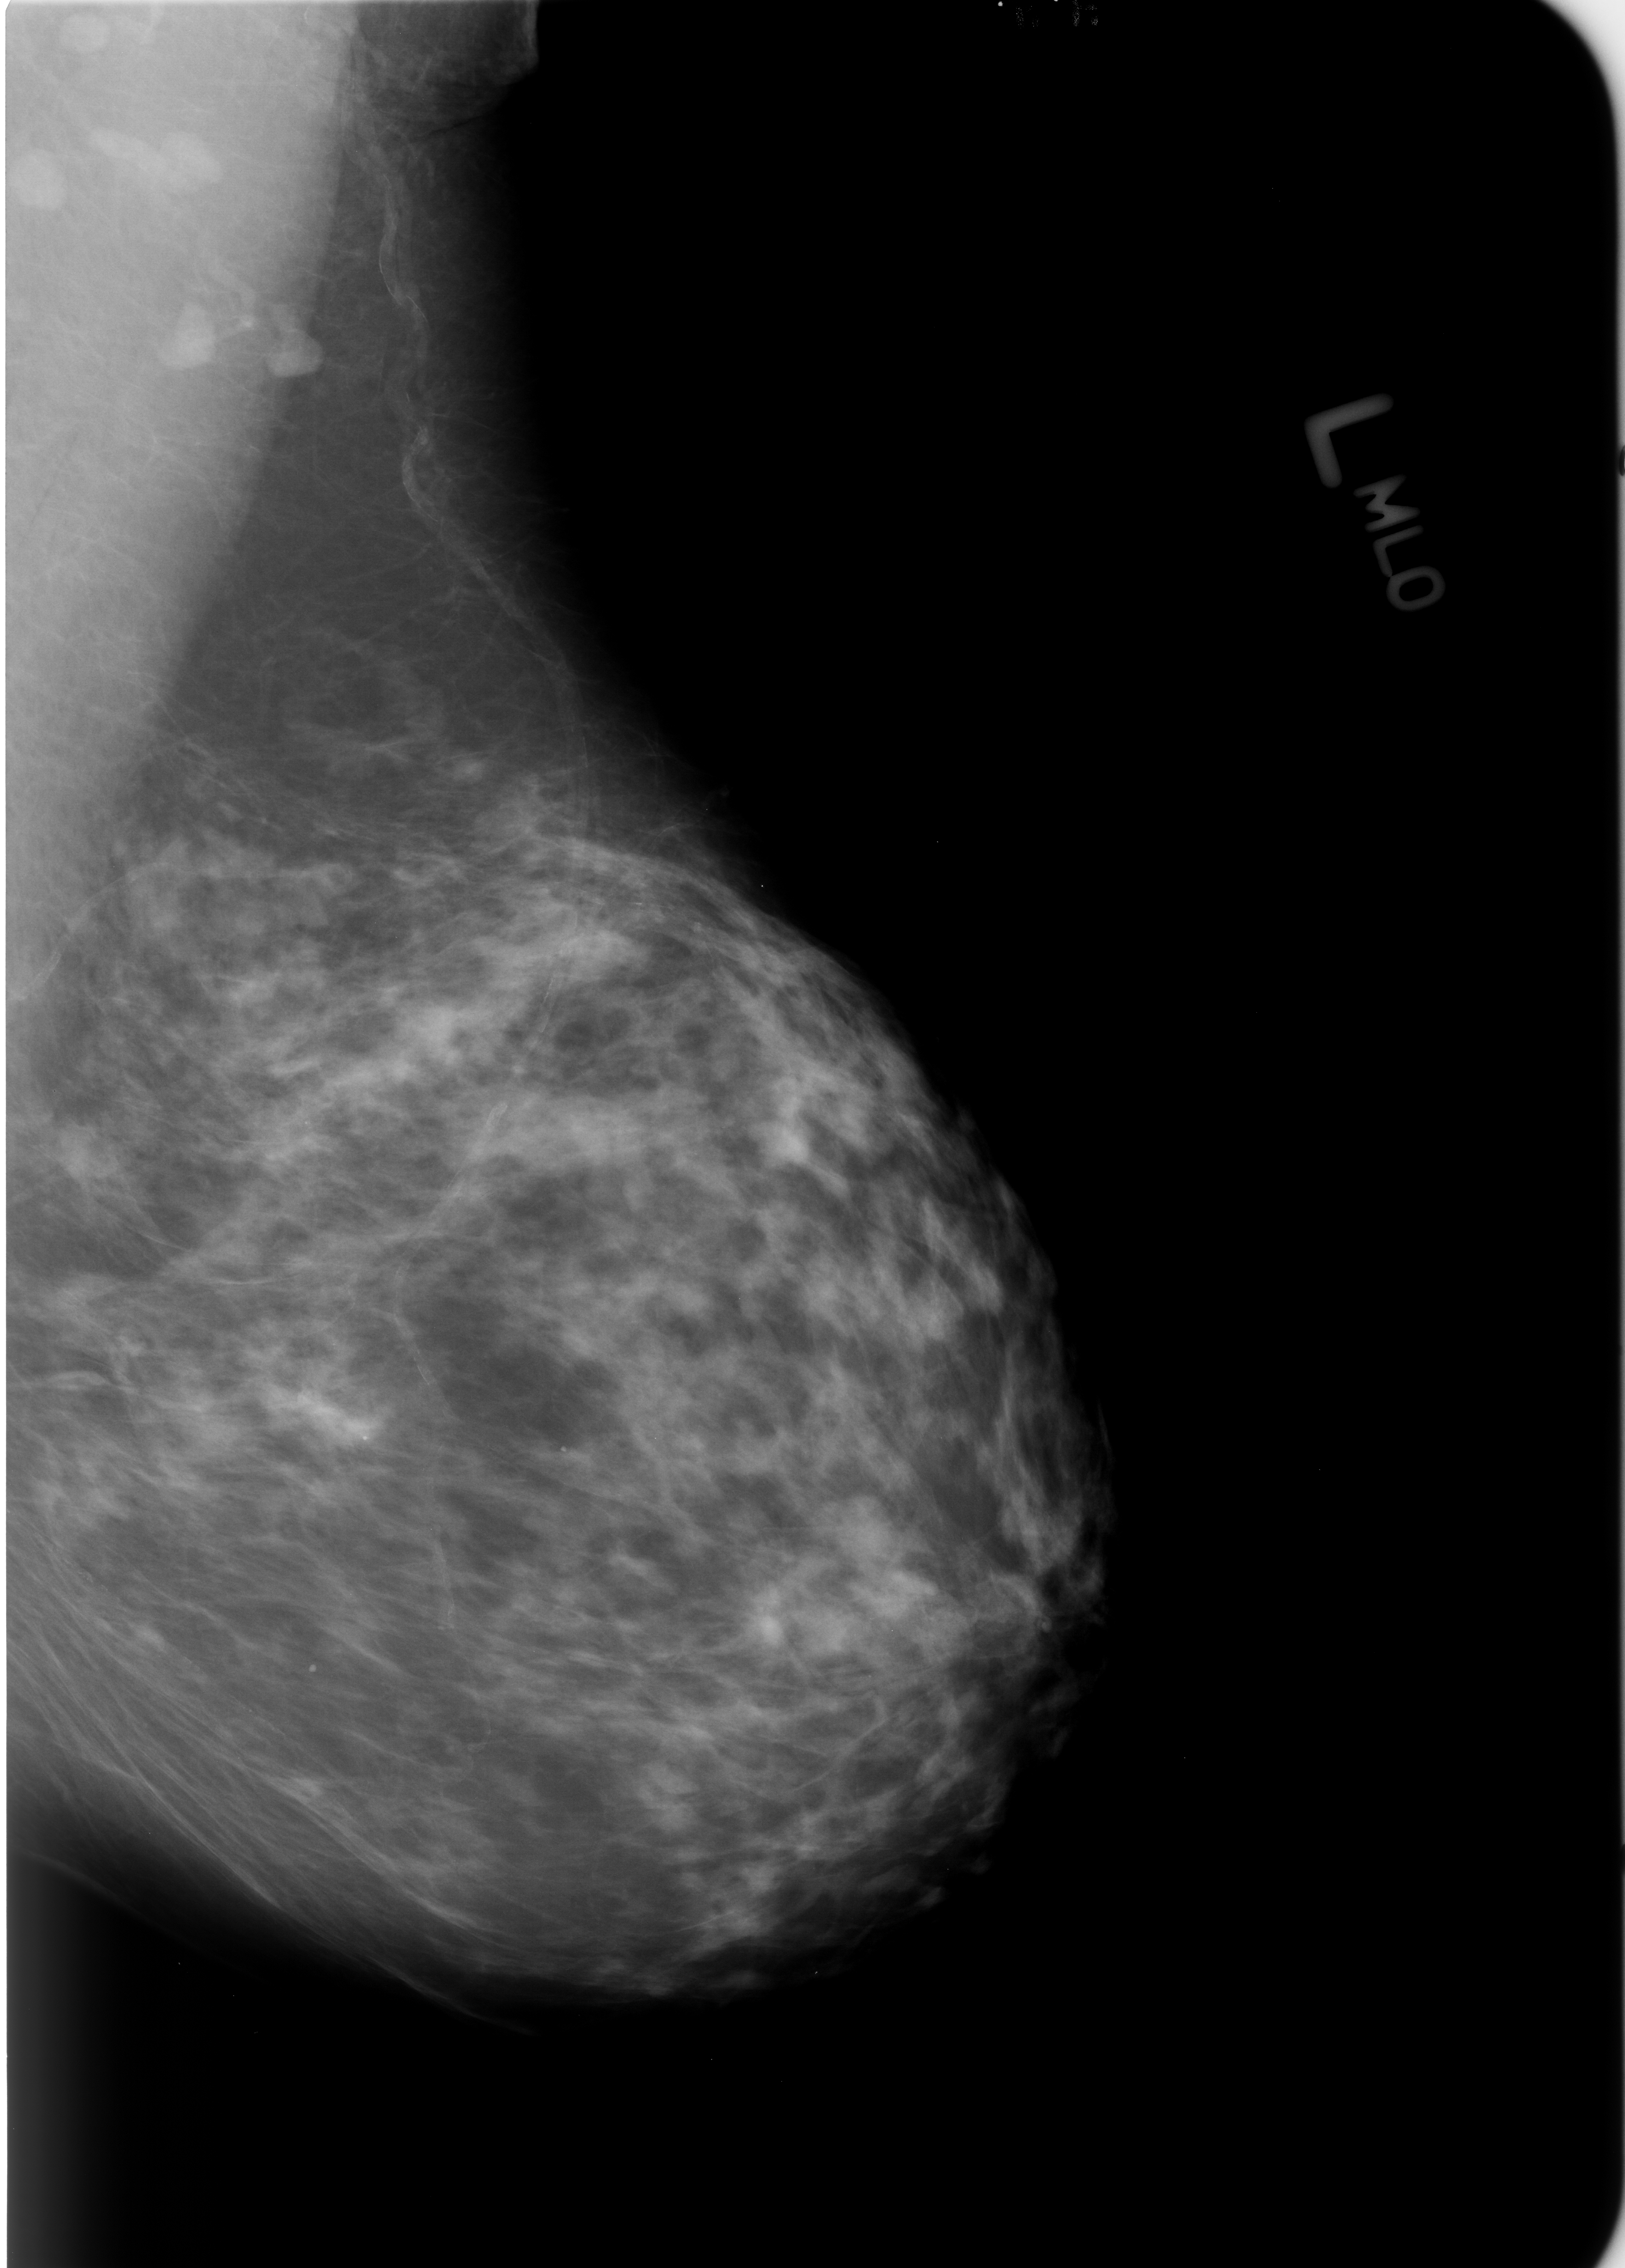
Mammogram (digitized film); left breast; mediolateral oblique (MLO) view; BI-RADS breast density category 2 (scale 1–4).
Marked findings (only marked abnormalities are described; nothing is implied about the rest of the image): Finding 1 of 4: calcifications, morphology punctate; BI-RADS assessment category 2; benign; no additional work-up was recommended (benign without callback). Finding 2 of 4: calcifications, morphology punctate; BI-RADS assessment category 2; subtlety rating 4 on a 1 (subtle) to 5 (obvious) scale; benign; no additional work-up was recommended (benign without callback). Finding 3 of 4: calcifications, morphology punctate; BI-RADS assessment category 2; subtlety rating 4 on a 1 (subtle) to 5 (obvious) scale; benign without callback (not worked up further). Finding 4 of 4: calcifications, morphology vascular; BI-RADS assessment category 2; benign; no additional work-up was recommended (benign without callback).